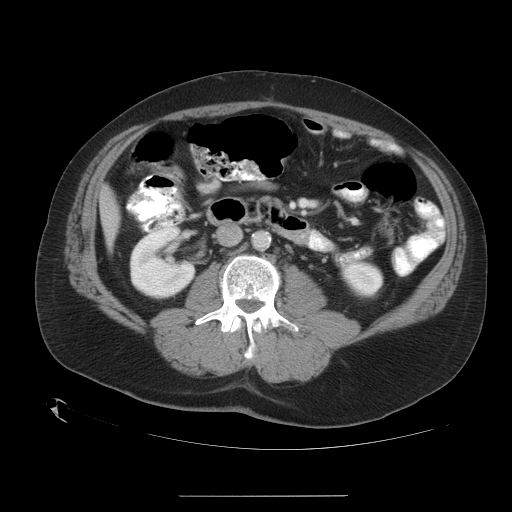
Contrast-enhanced abdominal CT, one axial slice. Slice 8 of 35 in the series (ordered by position). Reconstruction kernel STANDARD. 120 kVp. Intravenous contrast given. Soft-tissue window (W 400 / L 40 HU). 7.5 mm slice thickness. 512 × 512 image matrix, field of view 450 × 450 mm. Male patient, age 67 years. From the clinical record (not read from this slice): diagnosis: colorectal cancer liver metastases, imaged before liver resection; multiple liver metastases: no; largest metastasis: 2.3 cm; chemotherapy before resection: no.
Outlined on this slice (outlined manually by an expert reader):
- planned liver remnant (the part of the liver to remain after resection): box from (x=107, y=215) to (x=113, y=231) px